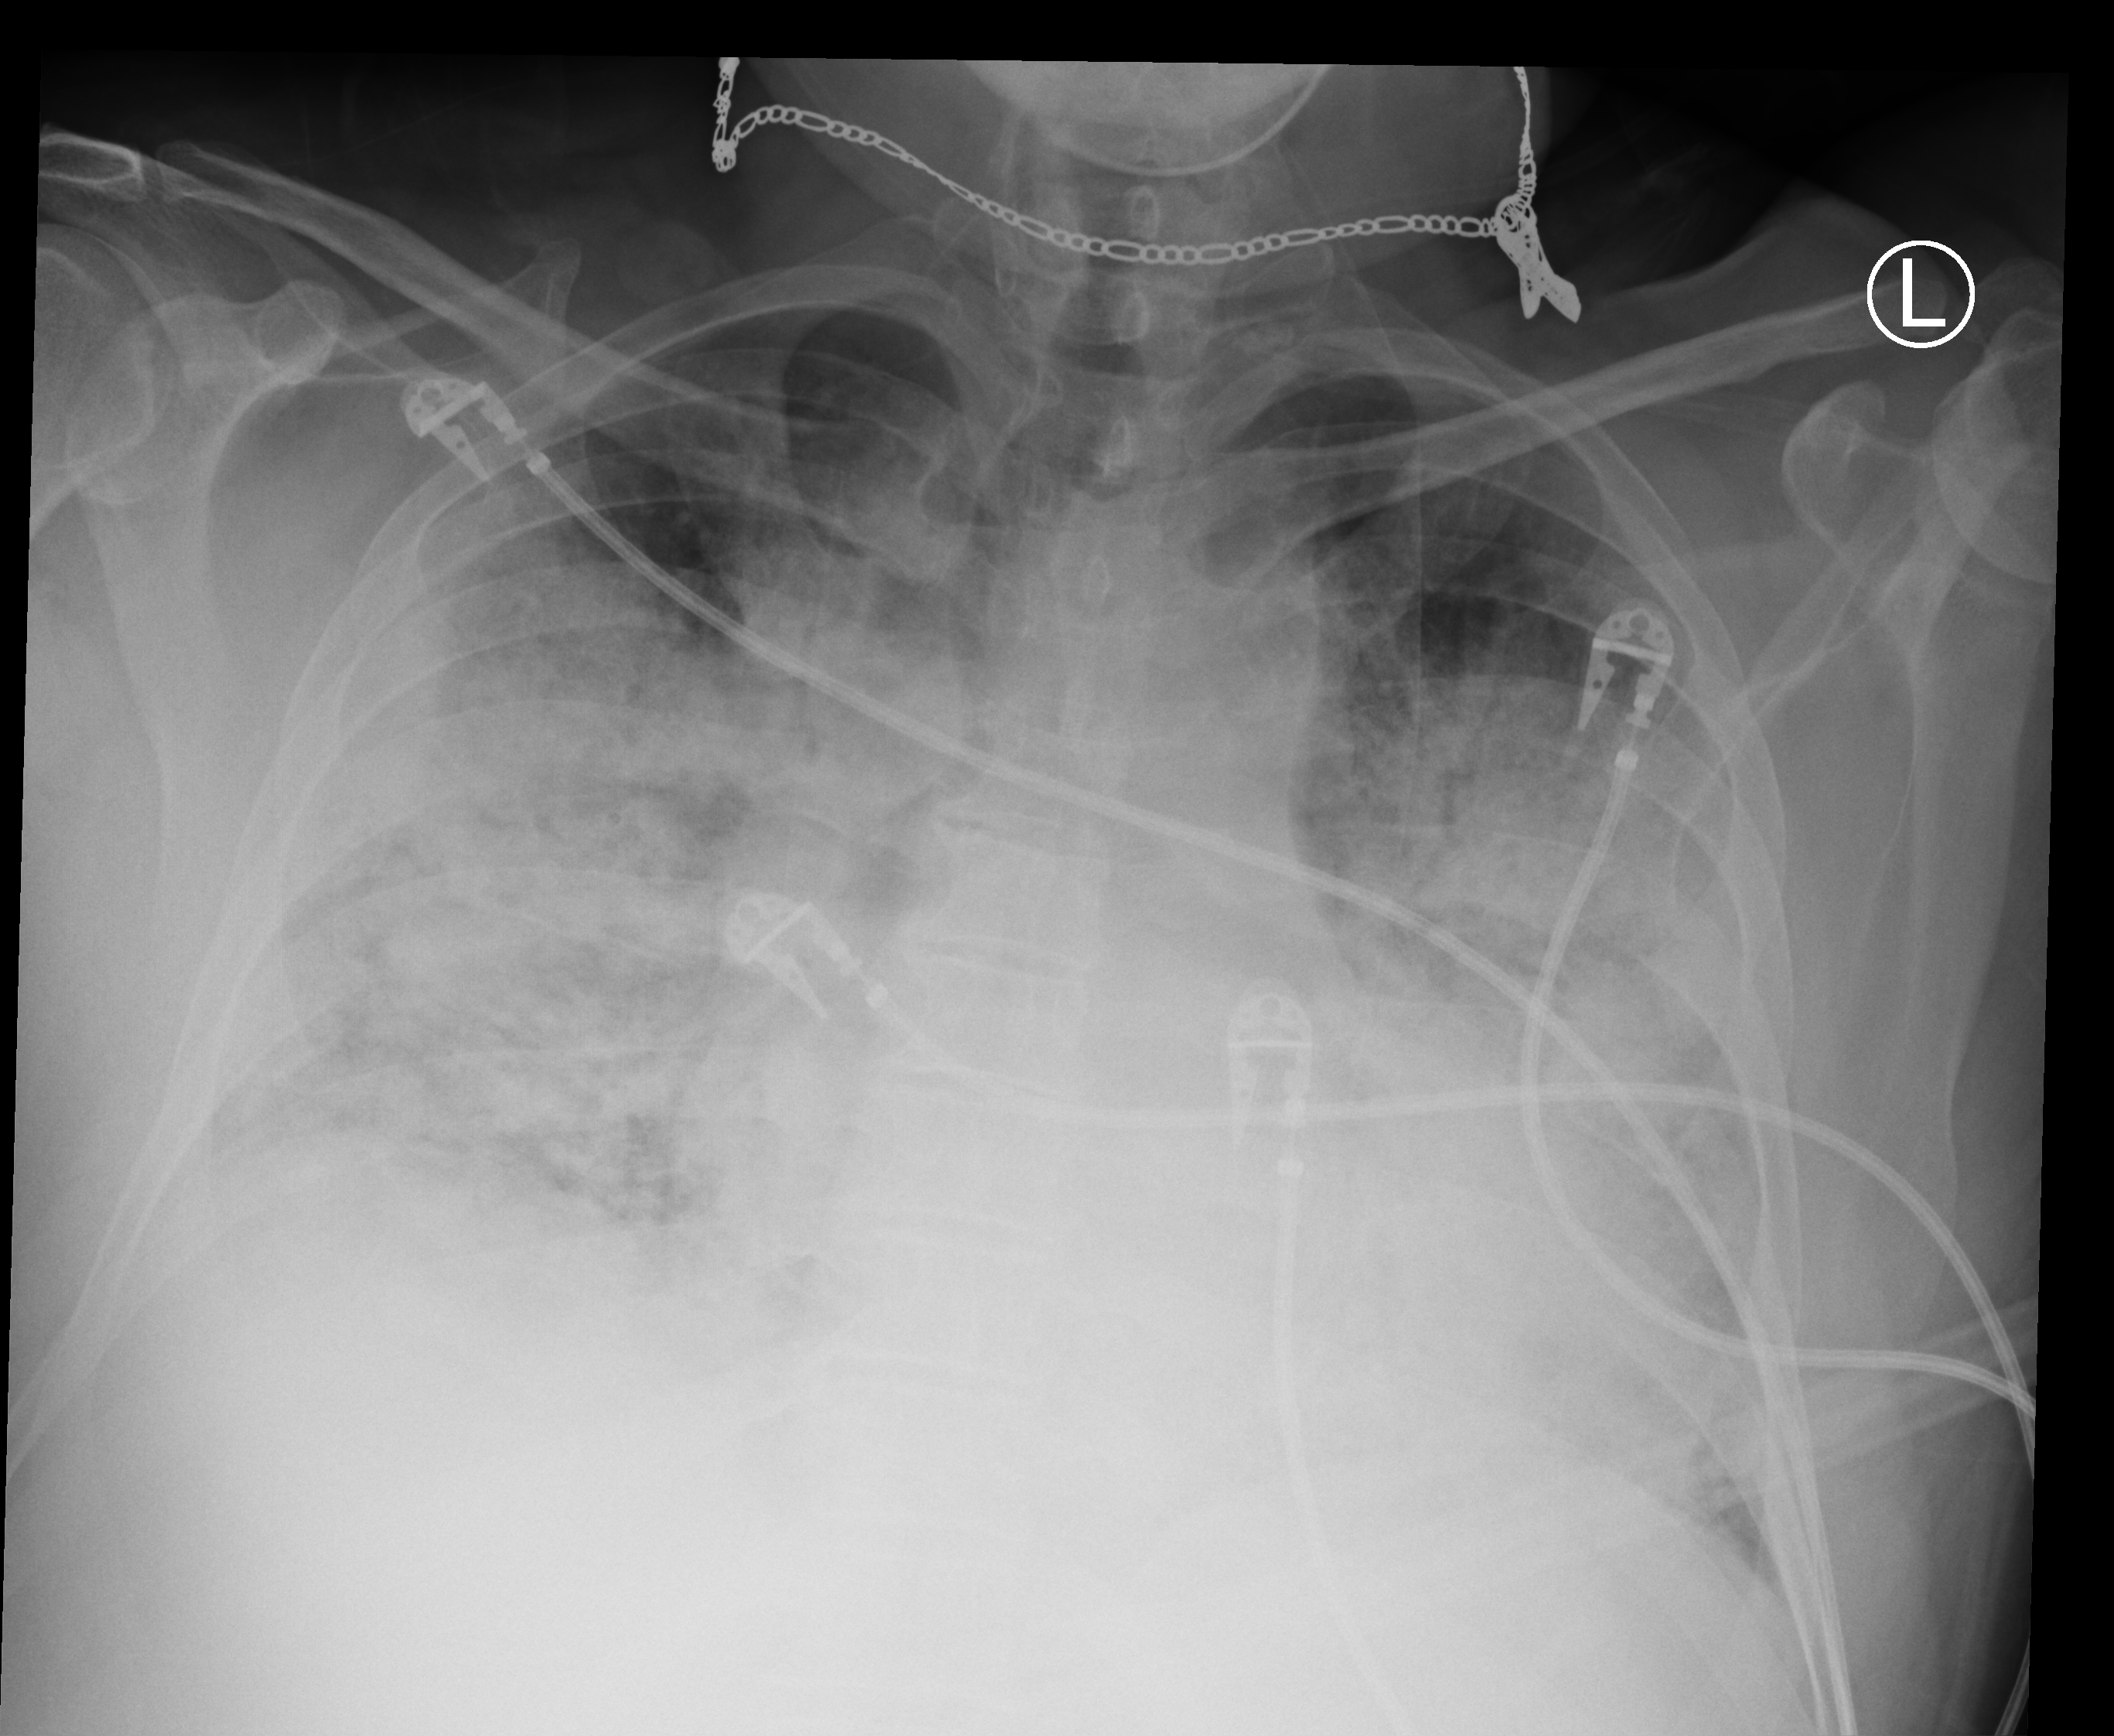
Chest X-ray (portable); anteroposterior (AP) projection. Male patient hospitalised with COVID-19, age 18–59 years.
From the hospital-stay record, not from the radiograph (when in the stay this image was taken is not recorded):
- mechanically ventilated during this hospital stay: yes
- admitted to intensive care during this hospital stay: yes
- COPD (admission record): no